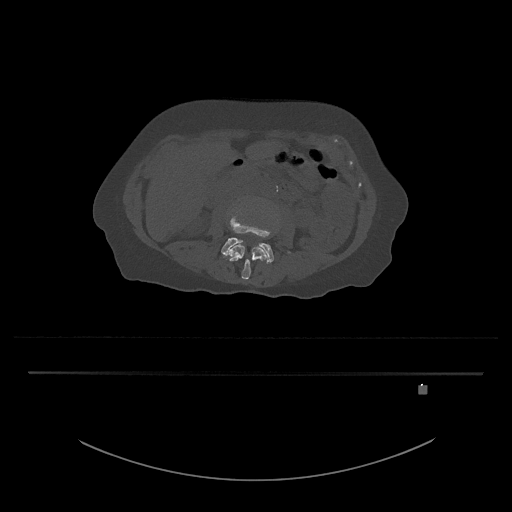
CT including the spine, one axial slice. Slice 395 of 797 in the series (ordered by position). Bone window (W 1800 / L 400 HU). 0.5 mm slice thickness. 512 × 512 image matrix, field of view 500 × 500 mm. Patient: female, 57 years. From the clinical record (not read from this slice): primary cancer: cervical.
Annotated regions visible in this slice (semi-automatic segmentation, software-assisted and operator-edited):
- L3 vertebra: box from (x=225, y=243) to (x=267, y=280) px
- L4 vertebra: (x=221, y=212)–(x=274, y=264)